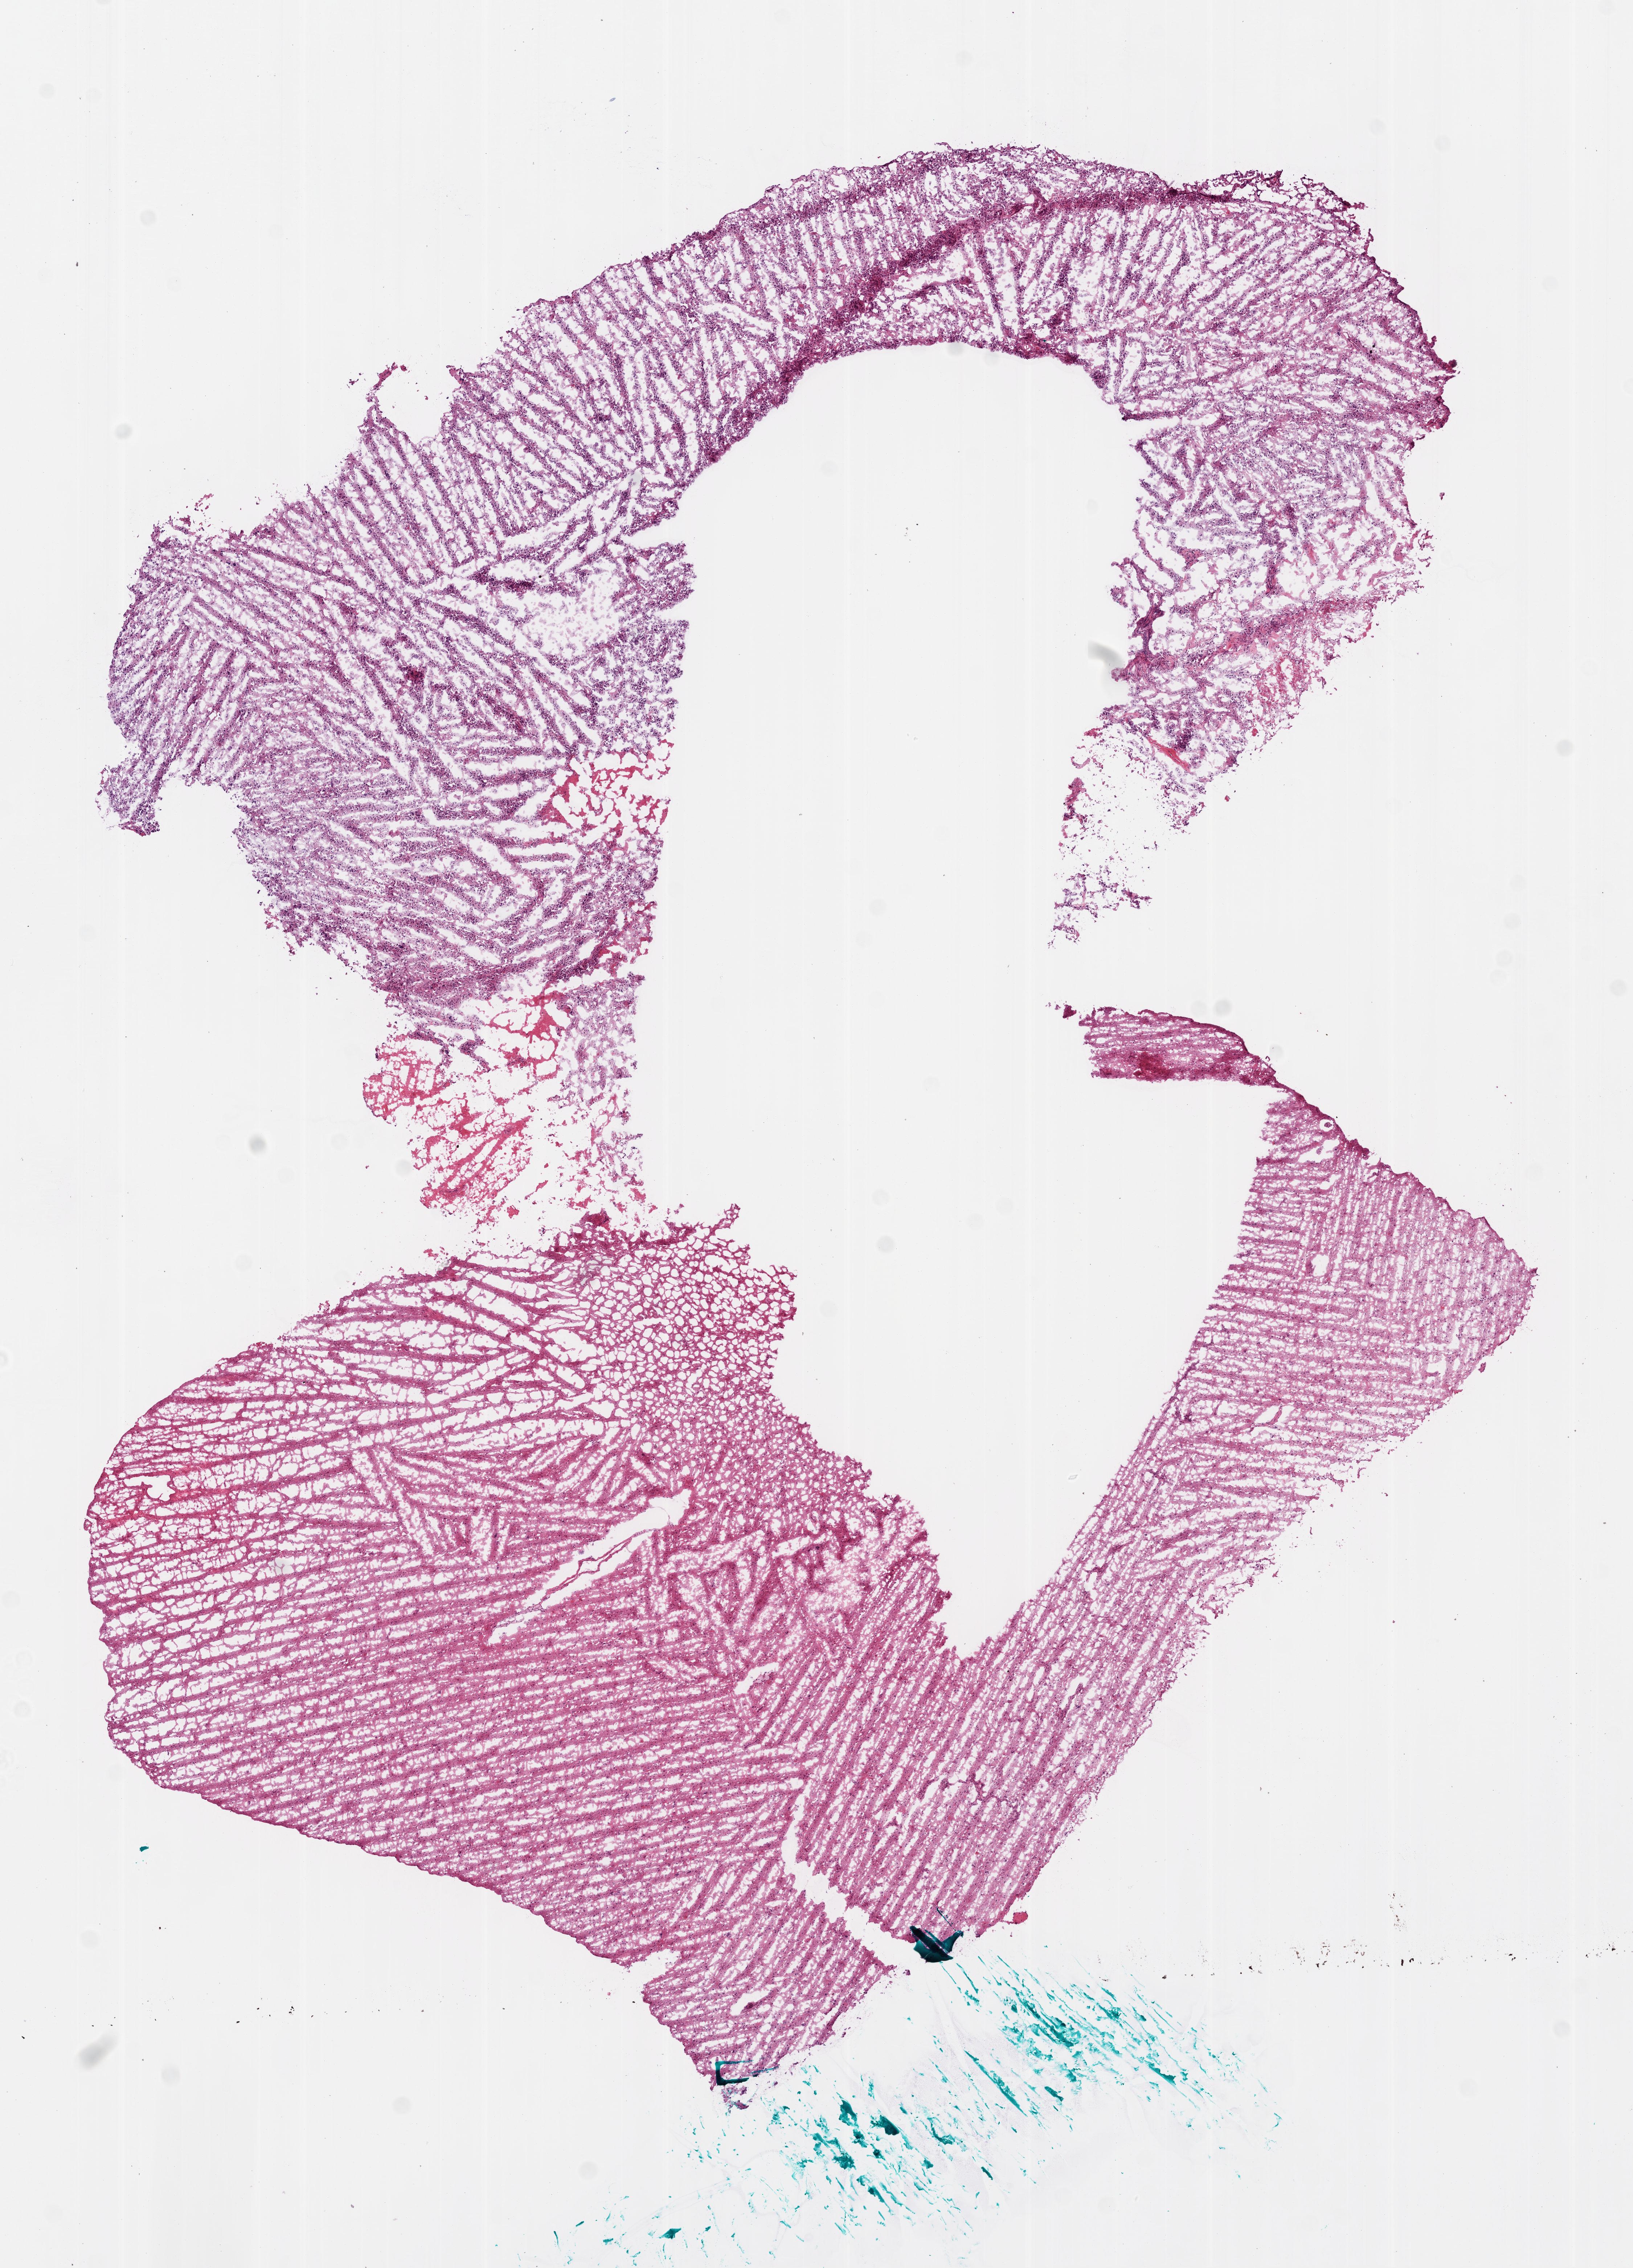
H&E-stained whole-slide image — a low-resolution overview of the entire scanned area, about 9.0 x 12.5 mm, frozen section from the bottom of the tissue portion, primary tumour sample from the brain. Female, age 38 years at initial diagnosis. Slide review estimates, as recorded: tumour cells 45%, tumour nuclei 80%, normal cells 0%, stromal cells 50%, necrosis 5%. Inflammatory infiltration, as recorded: lymphocyte infiltration 0%.
- diagnosis: Glioblastoma